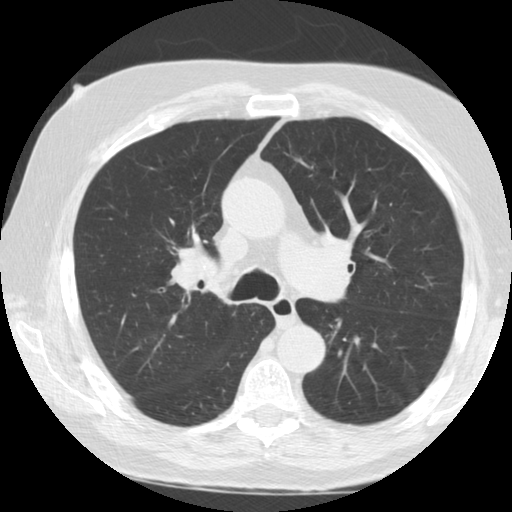
Low-dose screening chest CT, axial slice; second screening round (one year after baseline); lung window (W 1500 / L -600 HU); 2.5 mm slice thickness; 120 kVp; slice 42 of 110 in the series; 512 × 512 image matrix. Male participant, aged 72 years at enrolment.
• Lesion marked by an expert reader, bounding box [x1, y1, x2, y2] px = [160, 232, 228, 303].
• No non-calcified nodule or mass ≥4 mm was recorded by the screening reader at this exam.
• Official screen result: negative screen, minor abnormalities not suspicious for lung cancer.
• Later outcome: lung cancer diagnosed 415 days after this screen (after the third annual screen) — small cell carcinoma, NOS, right upper lobe, stage IV (AJCC 6th edition), 7 mm at pathology.